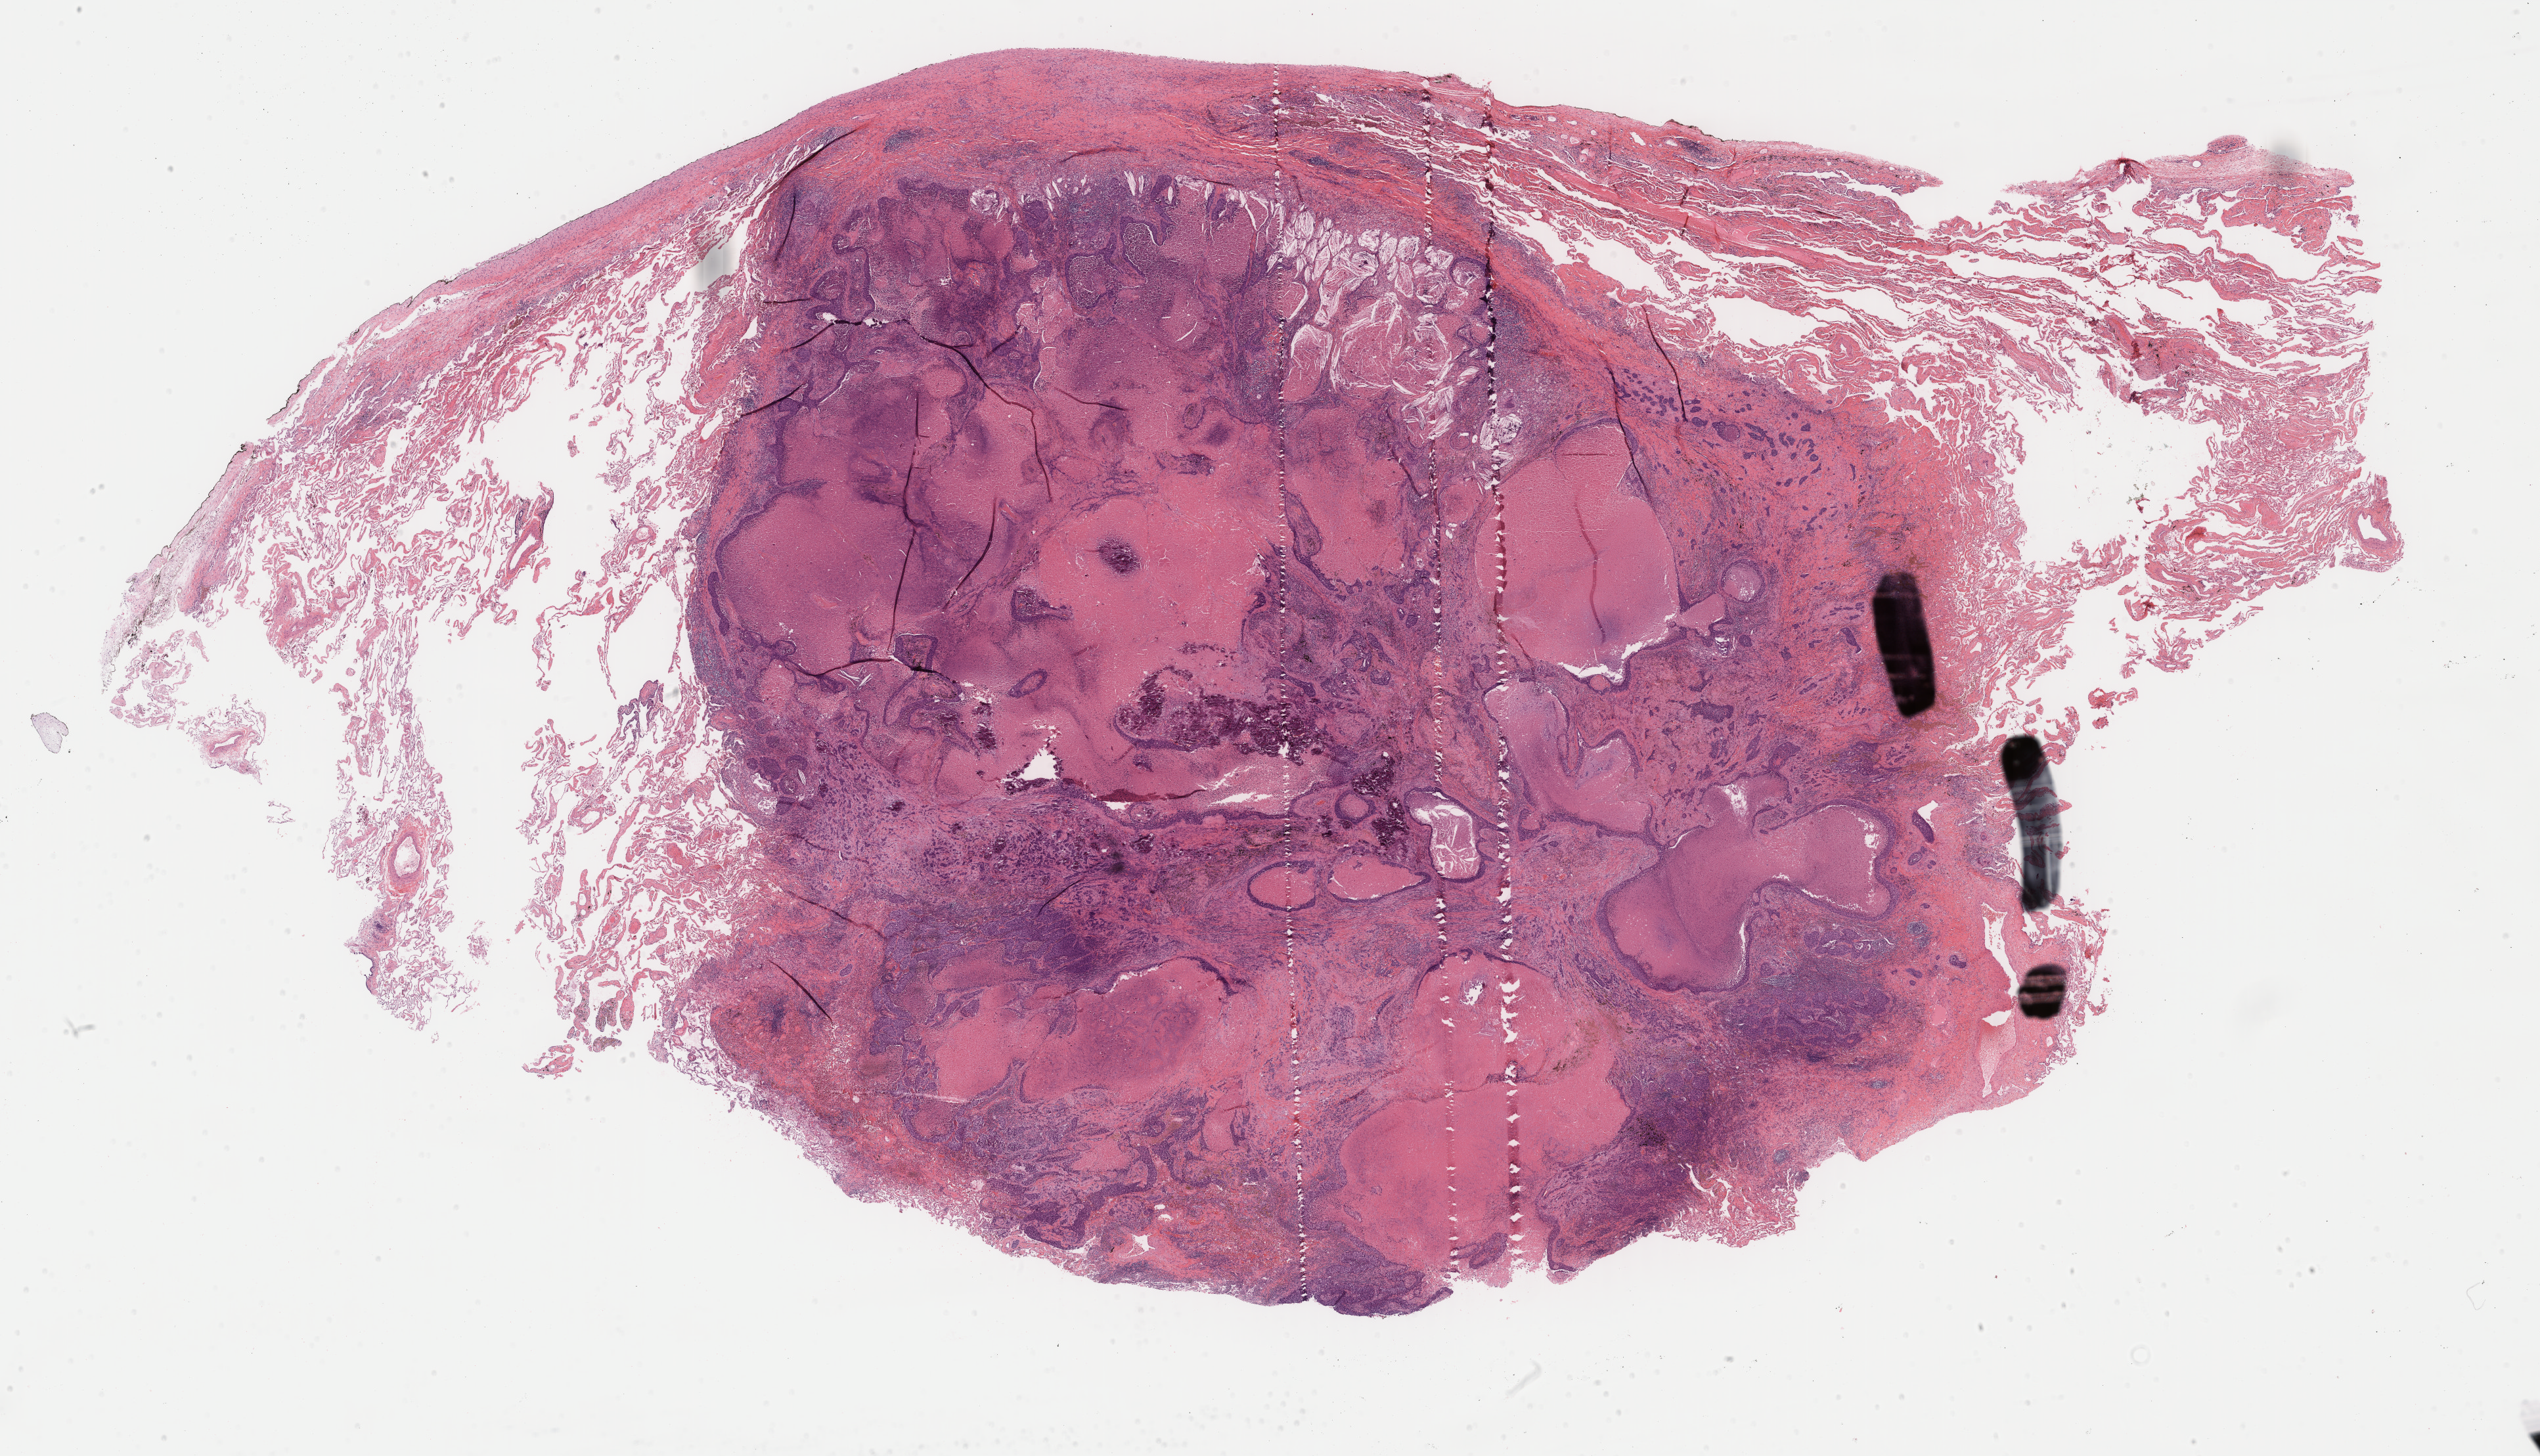
H&E whole-slide image, a low-resolution overview of the entire scanned area, about 30.7 x 17.6 mm; formalin-fixed paraffin-embedded (FFPE) diagnostic section; lung, primary tumour sample. Male patient; age at initial diagnosis 63 years.
Laterality: left. AJCC pathologic stage: IA. TNM: T1 N0 M0. Pathologic diagnosis: Squamous cell carcinoma, NOS (upper lobe, lung).